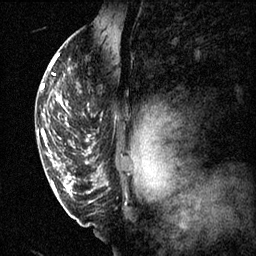
Breast MRI (dynamic contrast-enhanced), one sagittal slice. Slice 45 of 60 in the series (ordered by position). 3 images stored at this slice position (order not interpretable as contrast timing). 1.5 T. TE 4.2 ms, TR 11.1 ms. 2 mm slice thickness. 256 × 256 image matrix. Patient: female, 50 years.
Outlined on this slice (semi-automatic segmentation, software-assisted and operator-edited):
- analysis volume of interest (the breast-tissue region the enhancement analysis was run in; not a lesion): bounding box (x1, y1, x2, y2) in pixels: (68, 68, 100, 141)
- tumour enhancement mask (voxels above the 70 % enhancement threshold inside the analysis volume of interest): (68, 68, 91, 141)